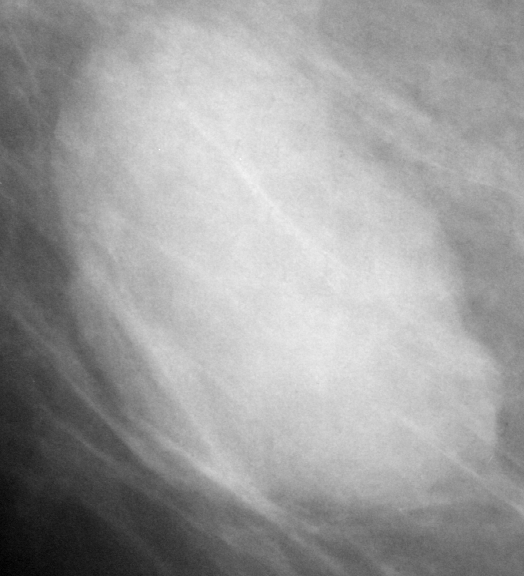
Cropped region of a digitized screen-film mammogram centred on a radiologist-marked abnormality, right breast, CC view, BI-RADS breast density category 2 (scale 1–4).
Marked abnormality: mass, shape oval, margins circumscribed; BI-RADS assessment category 3; pathology result (as recorded, not read from the image): benign.